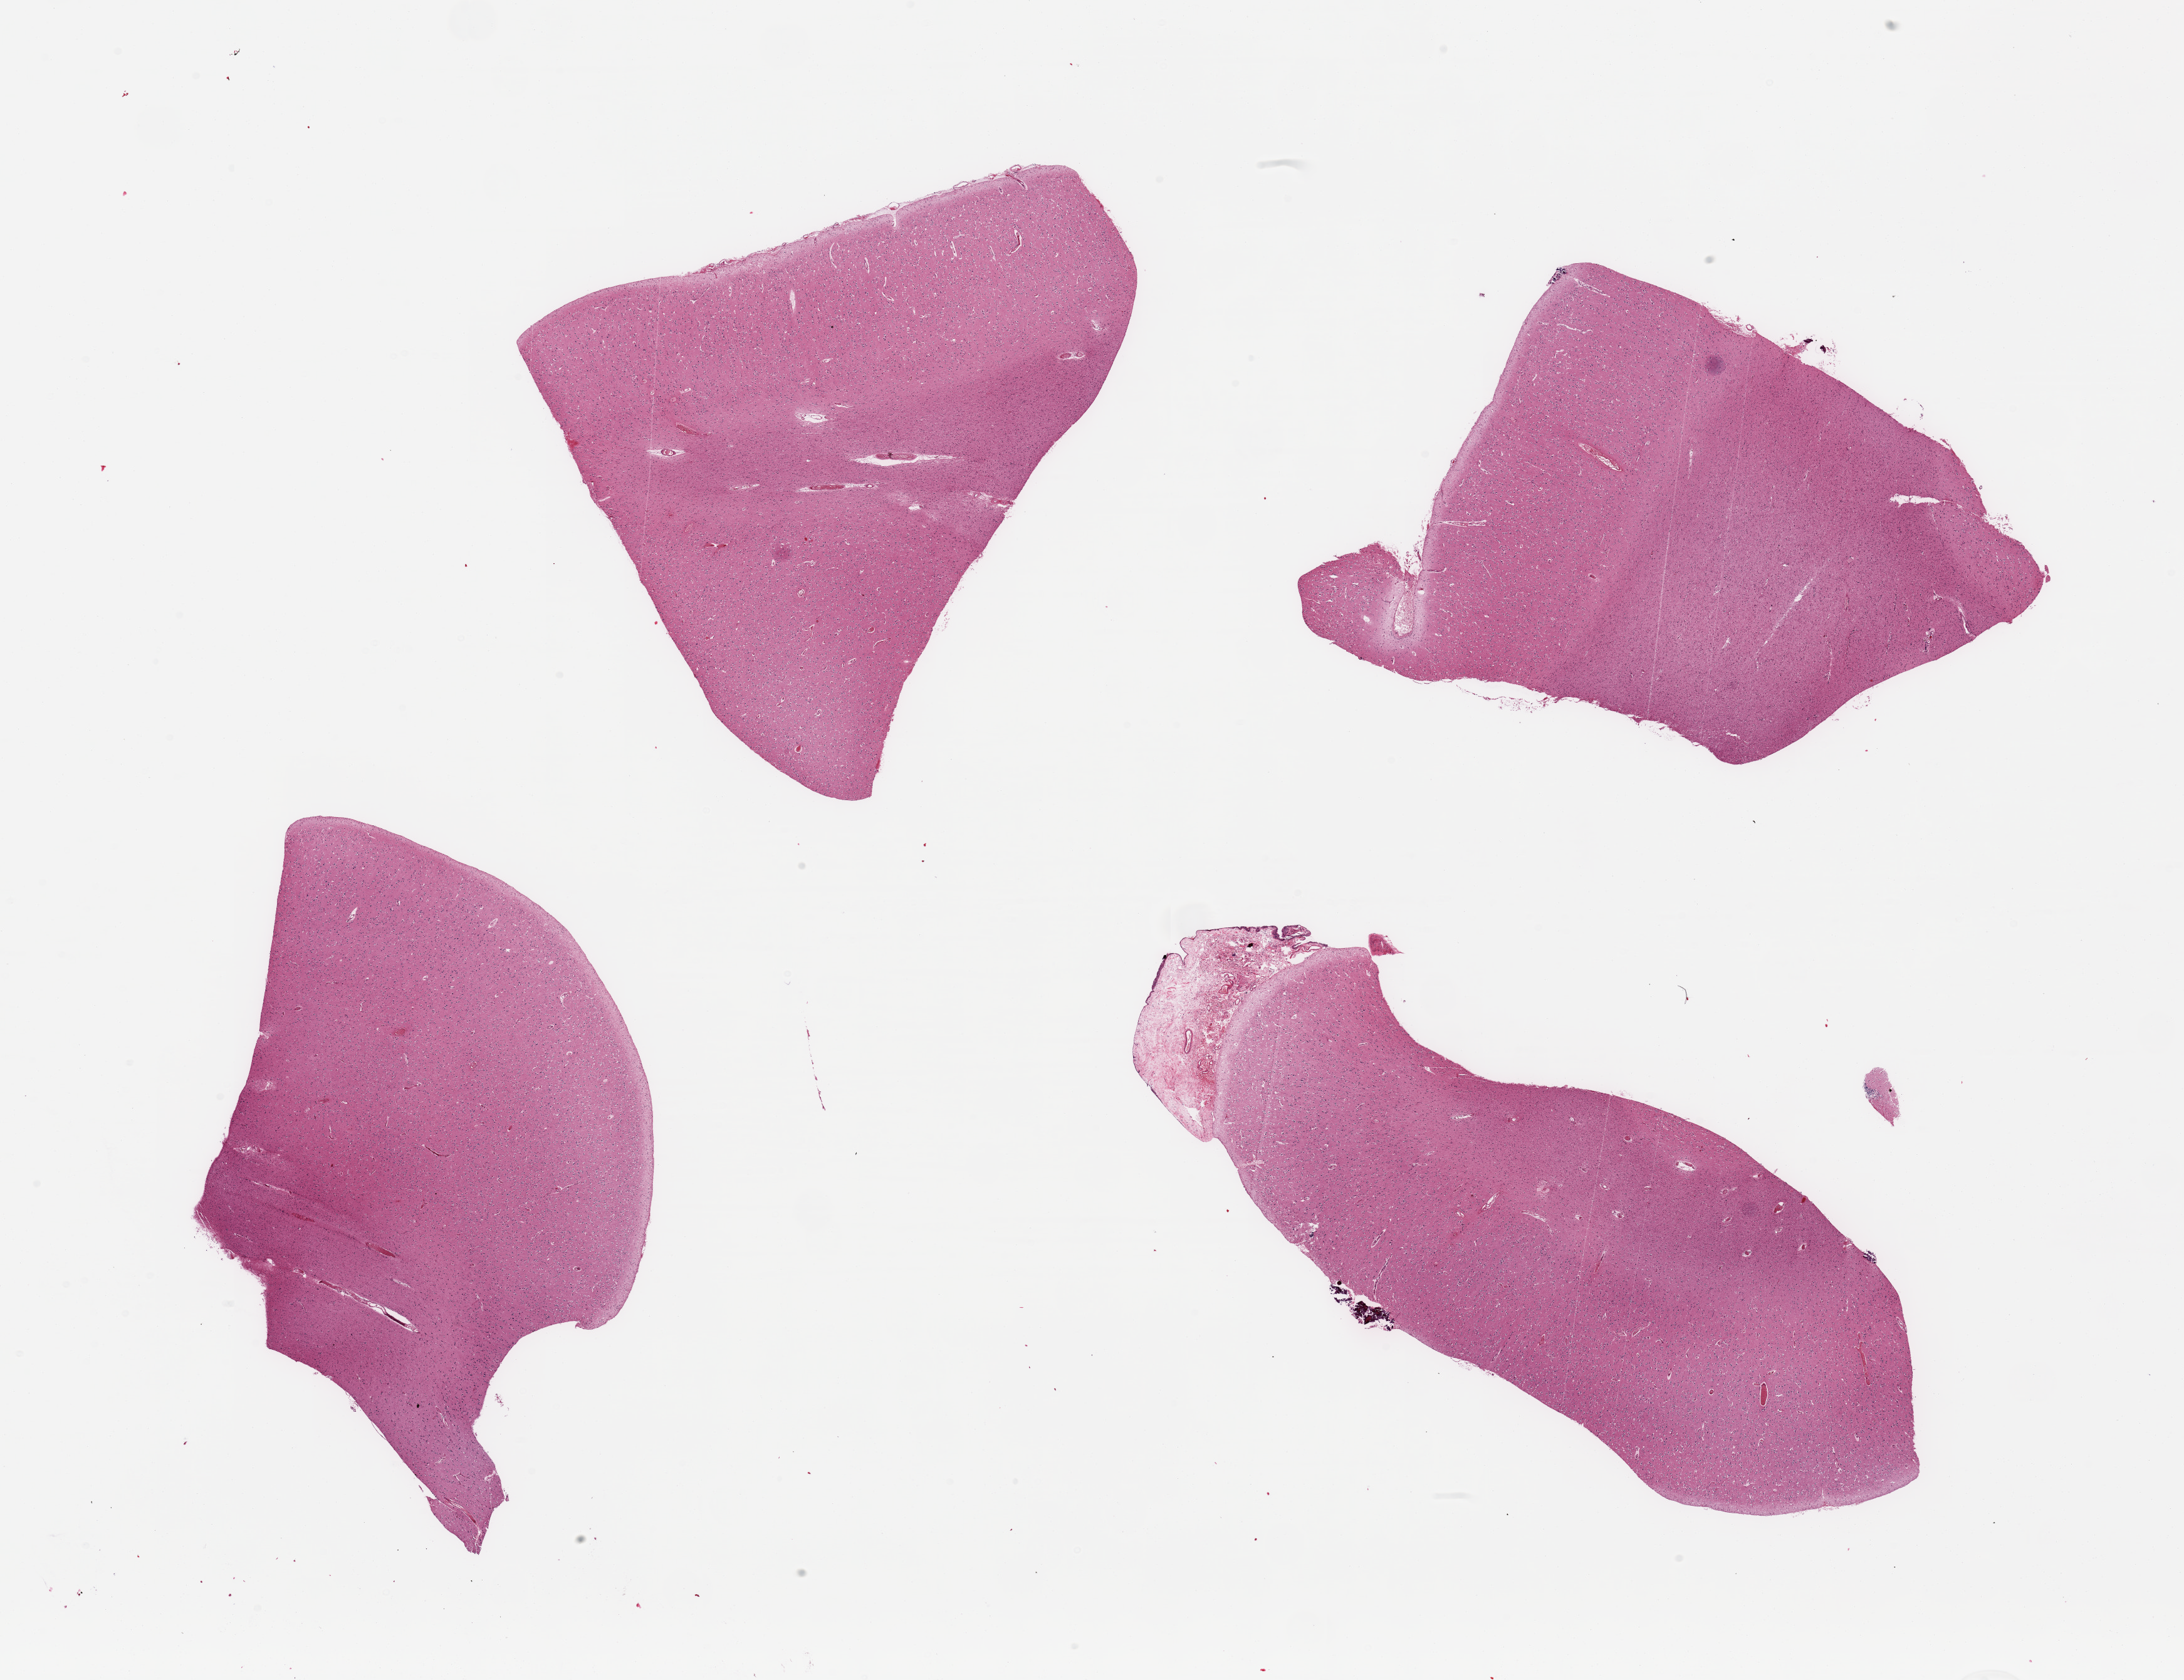
Whole-slide image, haematoxylin and eosin stain, brightfield, whole scanned area (about 27.6 x 21.2 mm, from a 20x scan) shown as a low-resolution overview, PAXgene-fixed paraffin-embedded (PFPE) section, sampled site (target tissue): cerebral cortex, tissue donor sample. Female donor.
Review note (as recorded): 4 pieces; 1 x 2.6mm meninges at edge of 1 piece.